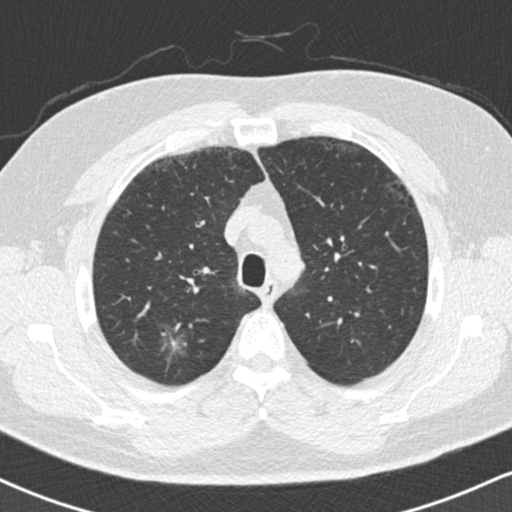
Low-dose screening chest CT, one axial slice. Slice 128 of 169 in the series (ordered by position). 120 kVp. Lung window (W 1500 / L -600 HU). 512 × 512 image matrix.
Structures marked on this image (expert manual segmentation):
- lesion 1 (tumor, upper lobe of right lung): bounding box [x1, y1, x2, y2] px = [162, 328, 184, 354]